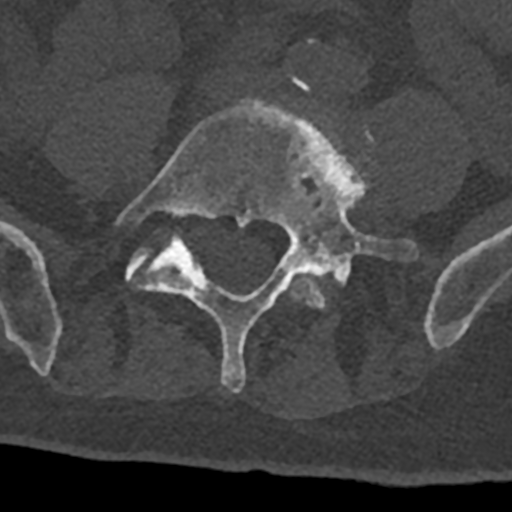
CT including the spine, one axial slice. Reconstruction kernel Br40s/3. 120 kVp. Bone window (W 1800 / L 400 HU). 0.5 mm slice thickness. 512 × 512 image matrix, field of view 160 × 160 mm. Male patient, age 74 years. From the clinical record (not read from this slice): primary cancer: renal; vertebrae with lytic lesions (as recorded): T10, L1, L2, L3, L4, L5.
Outlined on this slice (semi-automatically segmented with operator editing):
- L4 vertebra: bounding box (x1, y1, x2, y2) in pixels: (286, 76, 373, 309)
- L5 vertebra: (116, 98, 417, 392)